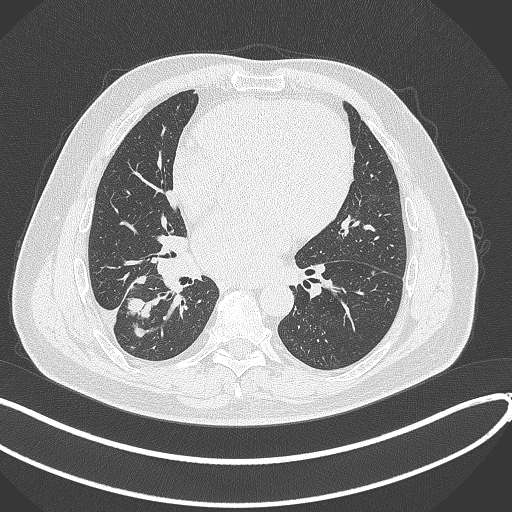
Chest CT, one axial slice. Position 167 of 360 along the scan axis. 120 kVp. Lung window (W 1500 / L -600 HU). 1 mm slice thickness. 512 × 512 image matrix, field of view 400 × 400 mm. Patient: male, 59 years.
Annotated regions visible in this slice (rectangle marked by the reading radiologist):
- lung tumour (recorded histology: adenocarcinoma): bounding box [x1, y1, x2, y2] px = [126, 274, 163, 339]